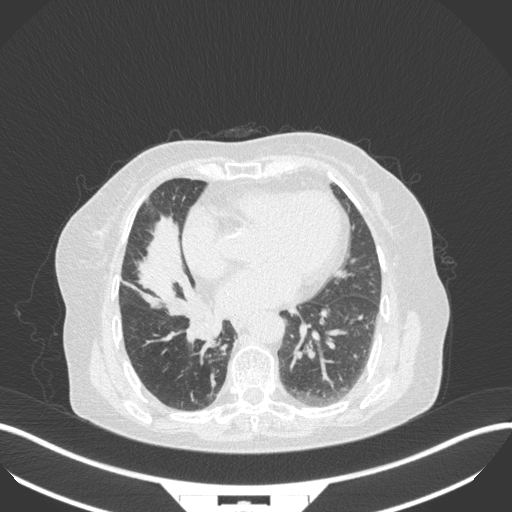
Chest CT, one axial slice; position 125 of 329 along the scan axis; lung window (W 1500 / L -600 HU); 1 mm slice thickness; 512 × 512 image matrix. Patient: female, 75 years. Case-level facts recorded for this patient, not image findings: clinical TNM (as recorded): T1b N0 M1a.
Annotated regions visible in this slice (rectangle marked by the reading radiologist):
- lung tumour (recorded histology: squamous cell carcinoma): bounding box <175,311,229,343> (left, top, right, bottom; pixels)